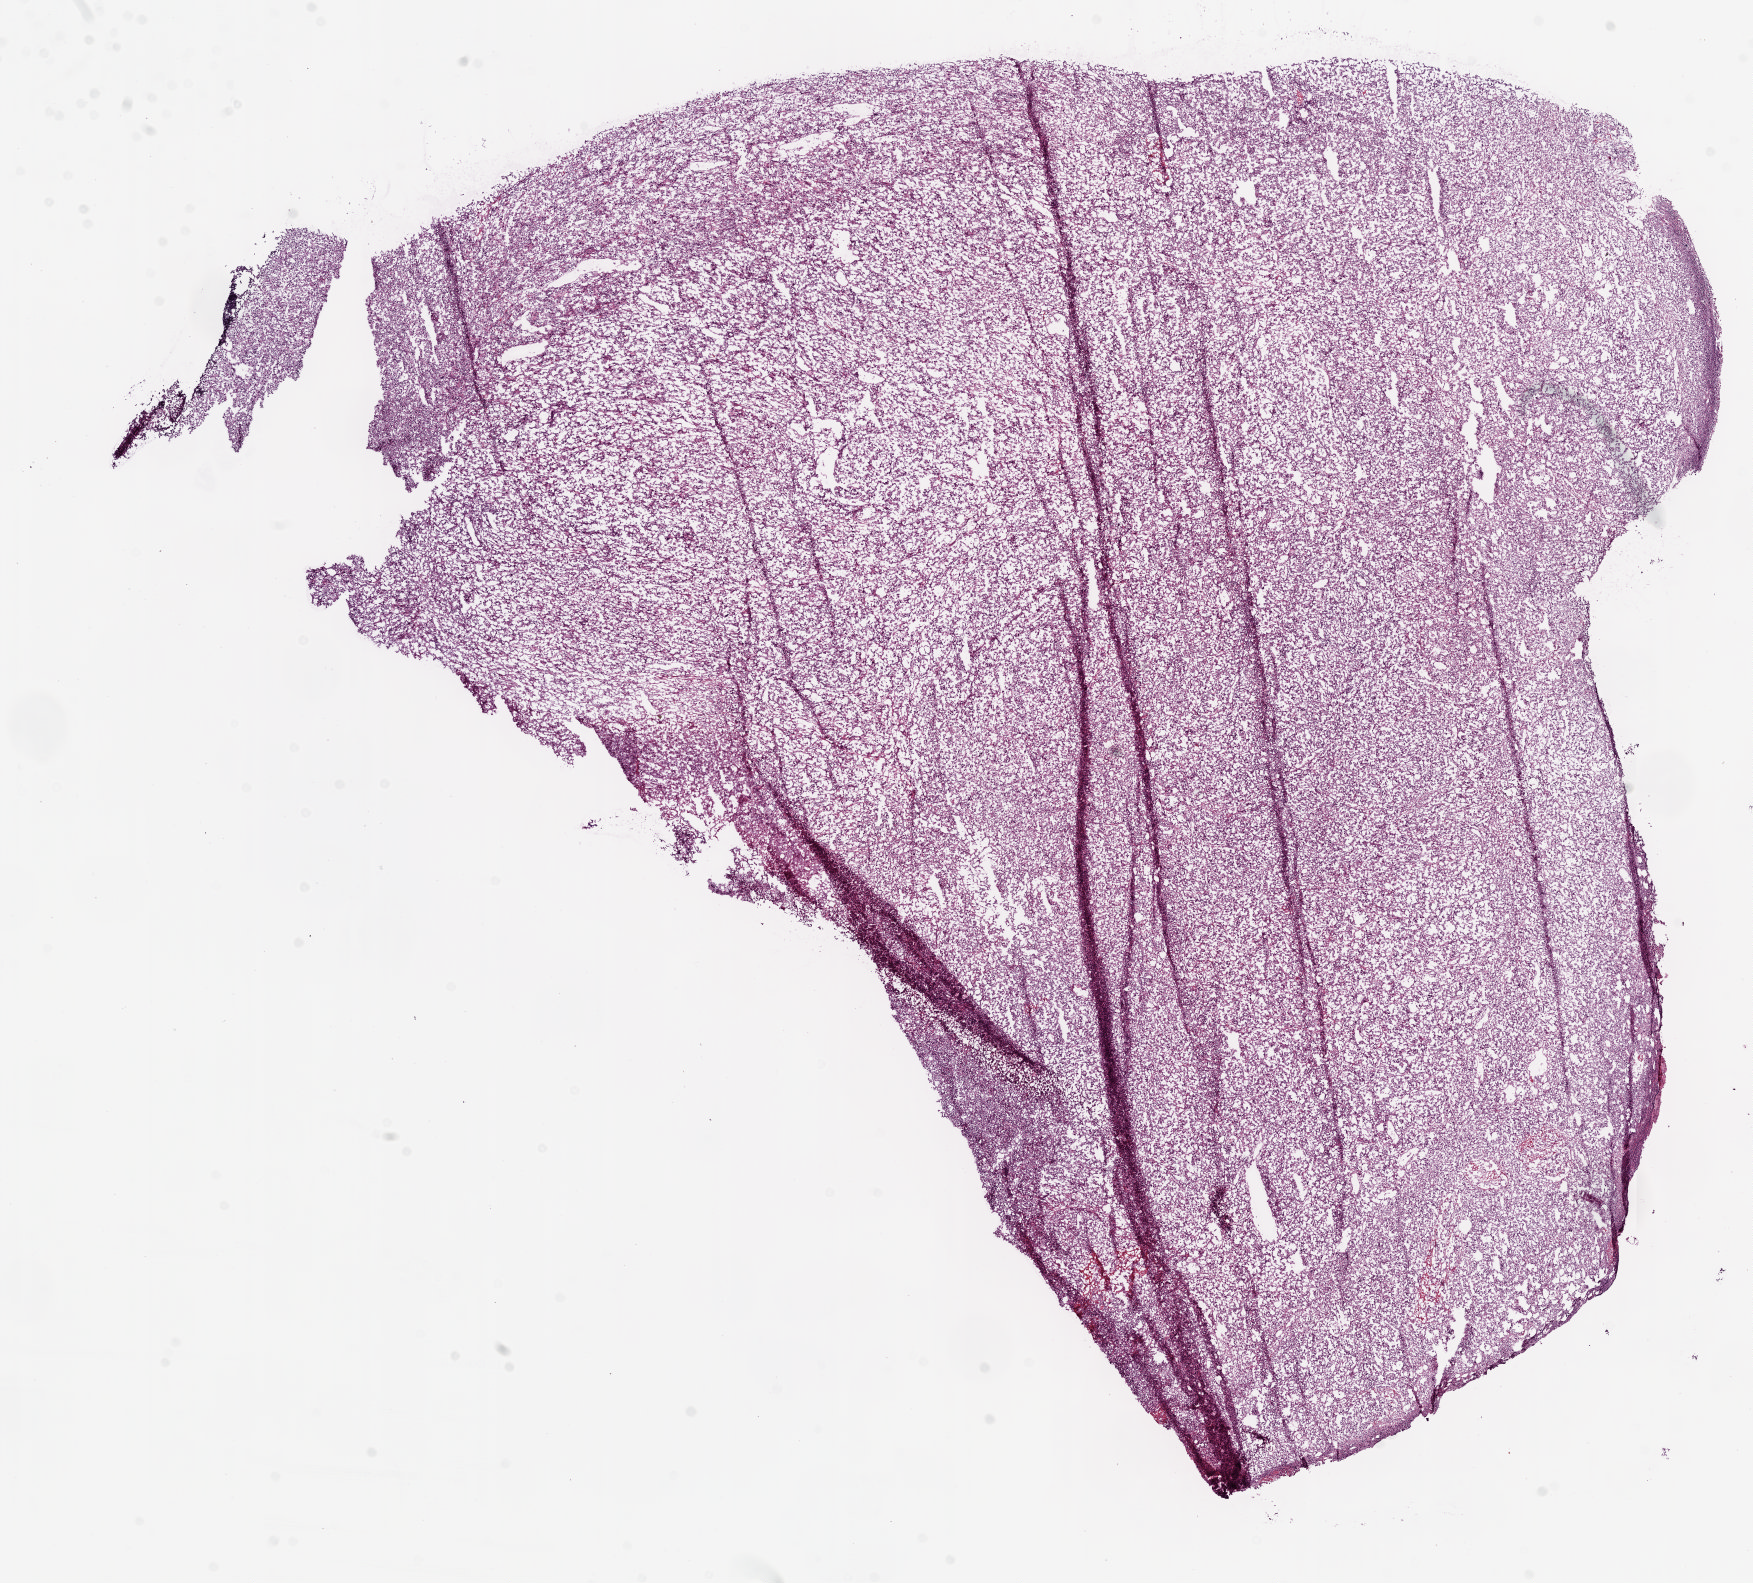
H&E-stained whole-slide image — low-resolution overview of the scanned area, about 14.1 x 12.7 mm, frozen section, kidney, primary tumour sample. Patient: male, age at initial diagnosis 75 years.
Histologic diagnosis: Clear cell adenocarcinoma, NOS.